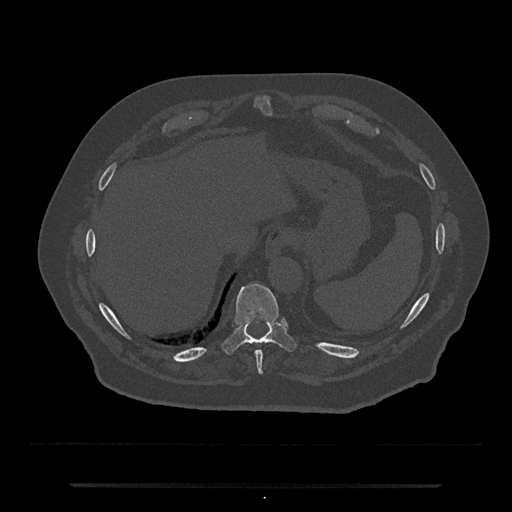
CT including the spine, one axial slice; slice 716 of 797 in the series (ordered by position); reconstruction kernel Br40s/3; bone window (W 1800 / L 400 HU); 512 × 512 image matrix, field of view 434 × 434 mm. Male patient, age 80 years. Case-level facts recorded for this patient, not image findings: primary cancer: prostate.
Structures marked on this image (semi-automatic segmentation, software-assisted and operator-edited):
- T10 vertebra: bounding box (x1, y1, x2, y2) in pixels: (222, 283, 296, 354)
- T9 vertebra: (256, 350, 263, 374)